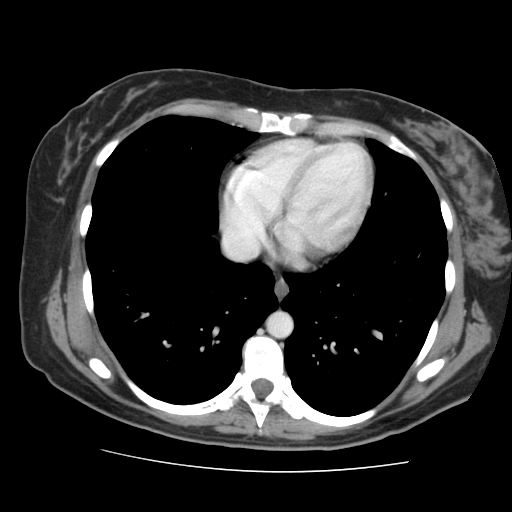
Contrast-enhanced abdominal CT, one axial slice. Intravenous contrast given. Soft-tissue window (W 400 / L 40 HU). 2.5 mm slice thickness. 512 × 512 image matrix. Female patient, age 46 years. From the clinical record (not read from this slice): diagnosis: colorectal cancer liver metastases, imaged before liver resection; multiple liver metastases: no.
Annotated regions visible in this slice (manually delineated by an expert):
- hepatic veins: bounding box <224,239,258,258> (left, top, right, bottom; pixels)